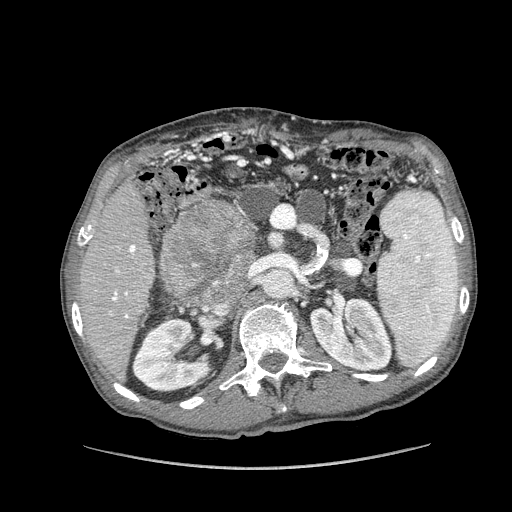
Contrast-enhanced abdominal CT (liver protocol), one axial slice; position 57 of 162 along the scan axis; reconstruction kernel STANDARD; soft-tissue window (W 400 / L 40 HU); 512 × 512 image matrix. Case-level facts recorded for this patient, not image findings: diagnosis: hepatocellular carcinoma (patient treated with transarterial chemoembolisation; whether this scan precedes or follows treatment is not stated here); TNM stage (as recorded): Stage-IIIA; Child-Pugh class: A; tumour nodularity: multinodular.
Outlined on this slice (semi-automatically segmented with operator editing):
- liver parenchyma outside the tumour (the mass and vessels are separate outlines, so this box may not span the whole liver): box from (x=80, y=180) to (x=154, y=377) px
- mass: (x=161, y=202)–(x=257, y=302)
- liver vessels: (x=112, y=245)–(x=136, y=318)